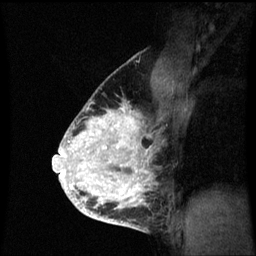
Breast MRI (dynamic contrast-enhanced), one sagittal slice; slice 43 of 60 in the series (ordered by position); dynamic contrast-enhanced series, image 2 of 3 at this slice position (ordered by acquisition); 1.5 T; TE 4.2 ms, TR 8.9 ms; 2 mm slice thickness; 256 × 256 image matrix. Patient: female, 35 years. From the clinical record (not read from this slice): setting: breast cancer imaged before/during neoadjuvant chemotherapy; receptor status: HR-positive, HER2-negative.
Annotated regions visible in this slice (semi-automatically segmented with operator editing):
- analysis volume of interest (the breast-tissue region the enhancement analysis was run in; not a lesion): box from (x=66, y=102) to (x=158, y=215) px
- tumour enhancement mask (voxels above the 70 % enhancement threshold inside the analysis volume of interest): (x=66, y=102)–(x=152, y=213)